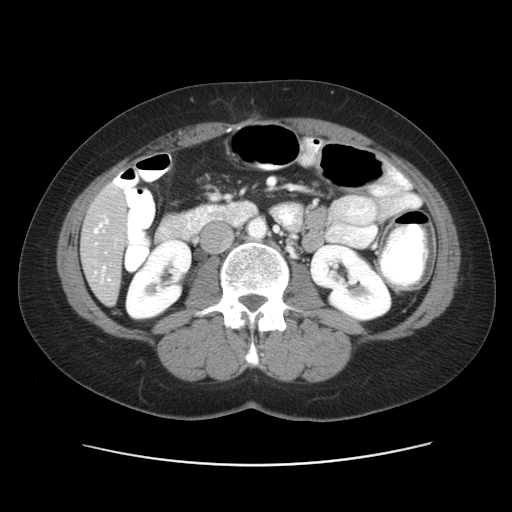
Contrast-enhanced abdominal CT, one axial slice; position 18 of 52 along the scan axis; soft-tissue window (W 400 / L 40 HU); 5 mm slice thickness; 512 × 512 image matrix. Female patient, age 48 years. Case-level facts recorded for this patient, not image findings: diagnosis: colorectal cancer liver metastases, imaged before liver resection.
Structures marked on this image (expert manual segmentation):
- hepatic veins: box from (x=95, y=217) to (x=110, y=281) px
- liver: (x=82, y=187)–(x=127, y=304)
- portal vein (with intrahepatic branches): (x=103, y=221)–(x=108, y=269)